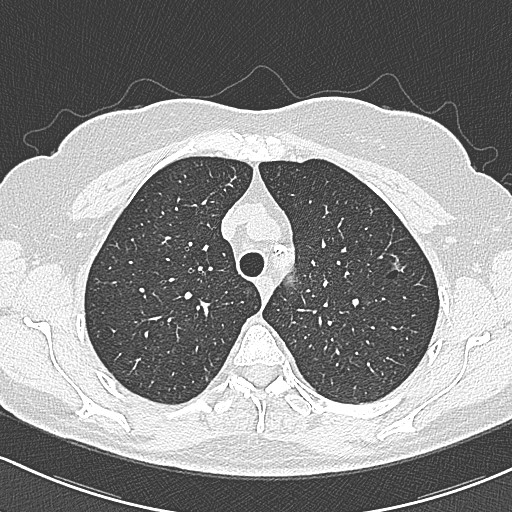
Chest CT (low-dose screening protocol), one axial image. Baseline annual screen. Lung window (W 1500 / L -600 HU). 1 mm slice thickness. 120 kVp. 512 × 512 image matrix, field of view 318 × 318 mm. Female, age 65 years at enrolment. Current smoker at enrolment.
Lesion marked by an expert reader, box from (x=375, y=240) to (x=415, y=285) px. The screening reader recorded 3 non-calcified nodules or masses ≥4 mm on this exam (left upper lobe, left upper lobe, right upper lobe); which of them this box marks is not recorded. Lung cancer was diagnosed 390 days after this screen (after the second annual screen): bronchiolo-alveolar carcinoma, non-mucinous, left upper lobe, stage IA (AJCC 6th edition), 10 mm at pathology.